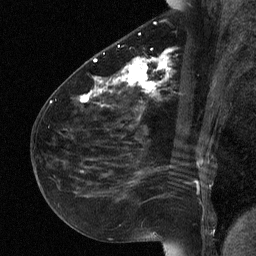
Breast MRI (dynamic contrast-enhanced), one sagittal slice; slice 31 of 64 in the series (ordered by position); dynamic contrast-enhanced study with each time point stored as its own series, time point 2 of 3 at this slice position (early post-contrast, ordered by acquisition time); 1.5 T; TE 4.8 ms, TR 27 ms; 2 mm slice thickness; 256 × 256 image matrix, field of view 180 × 180 mm. Patient: female, 51 years. Case-level facts recorded for this patient, not image findings: setting: breast cancer imaged before/during neoadjuvant chemotherapy; receptor status: HR-positive, HER2-negative.
Structures marked on this image (semi-automatic segmentation, software-assisted and operator-edited):
- analysis volume of interest (the breast-tissue region the enhancement analysis was run in; not a lesion): box from (x=72, y=34) to (x=182, y=118) px
- tumour enhancement mask (voxels above the 90 % enhancement threshold inside the analysis volume of interest): (x=80, y=57)–(x=167, y=102)